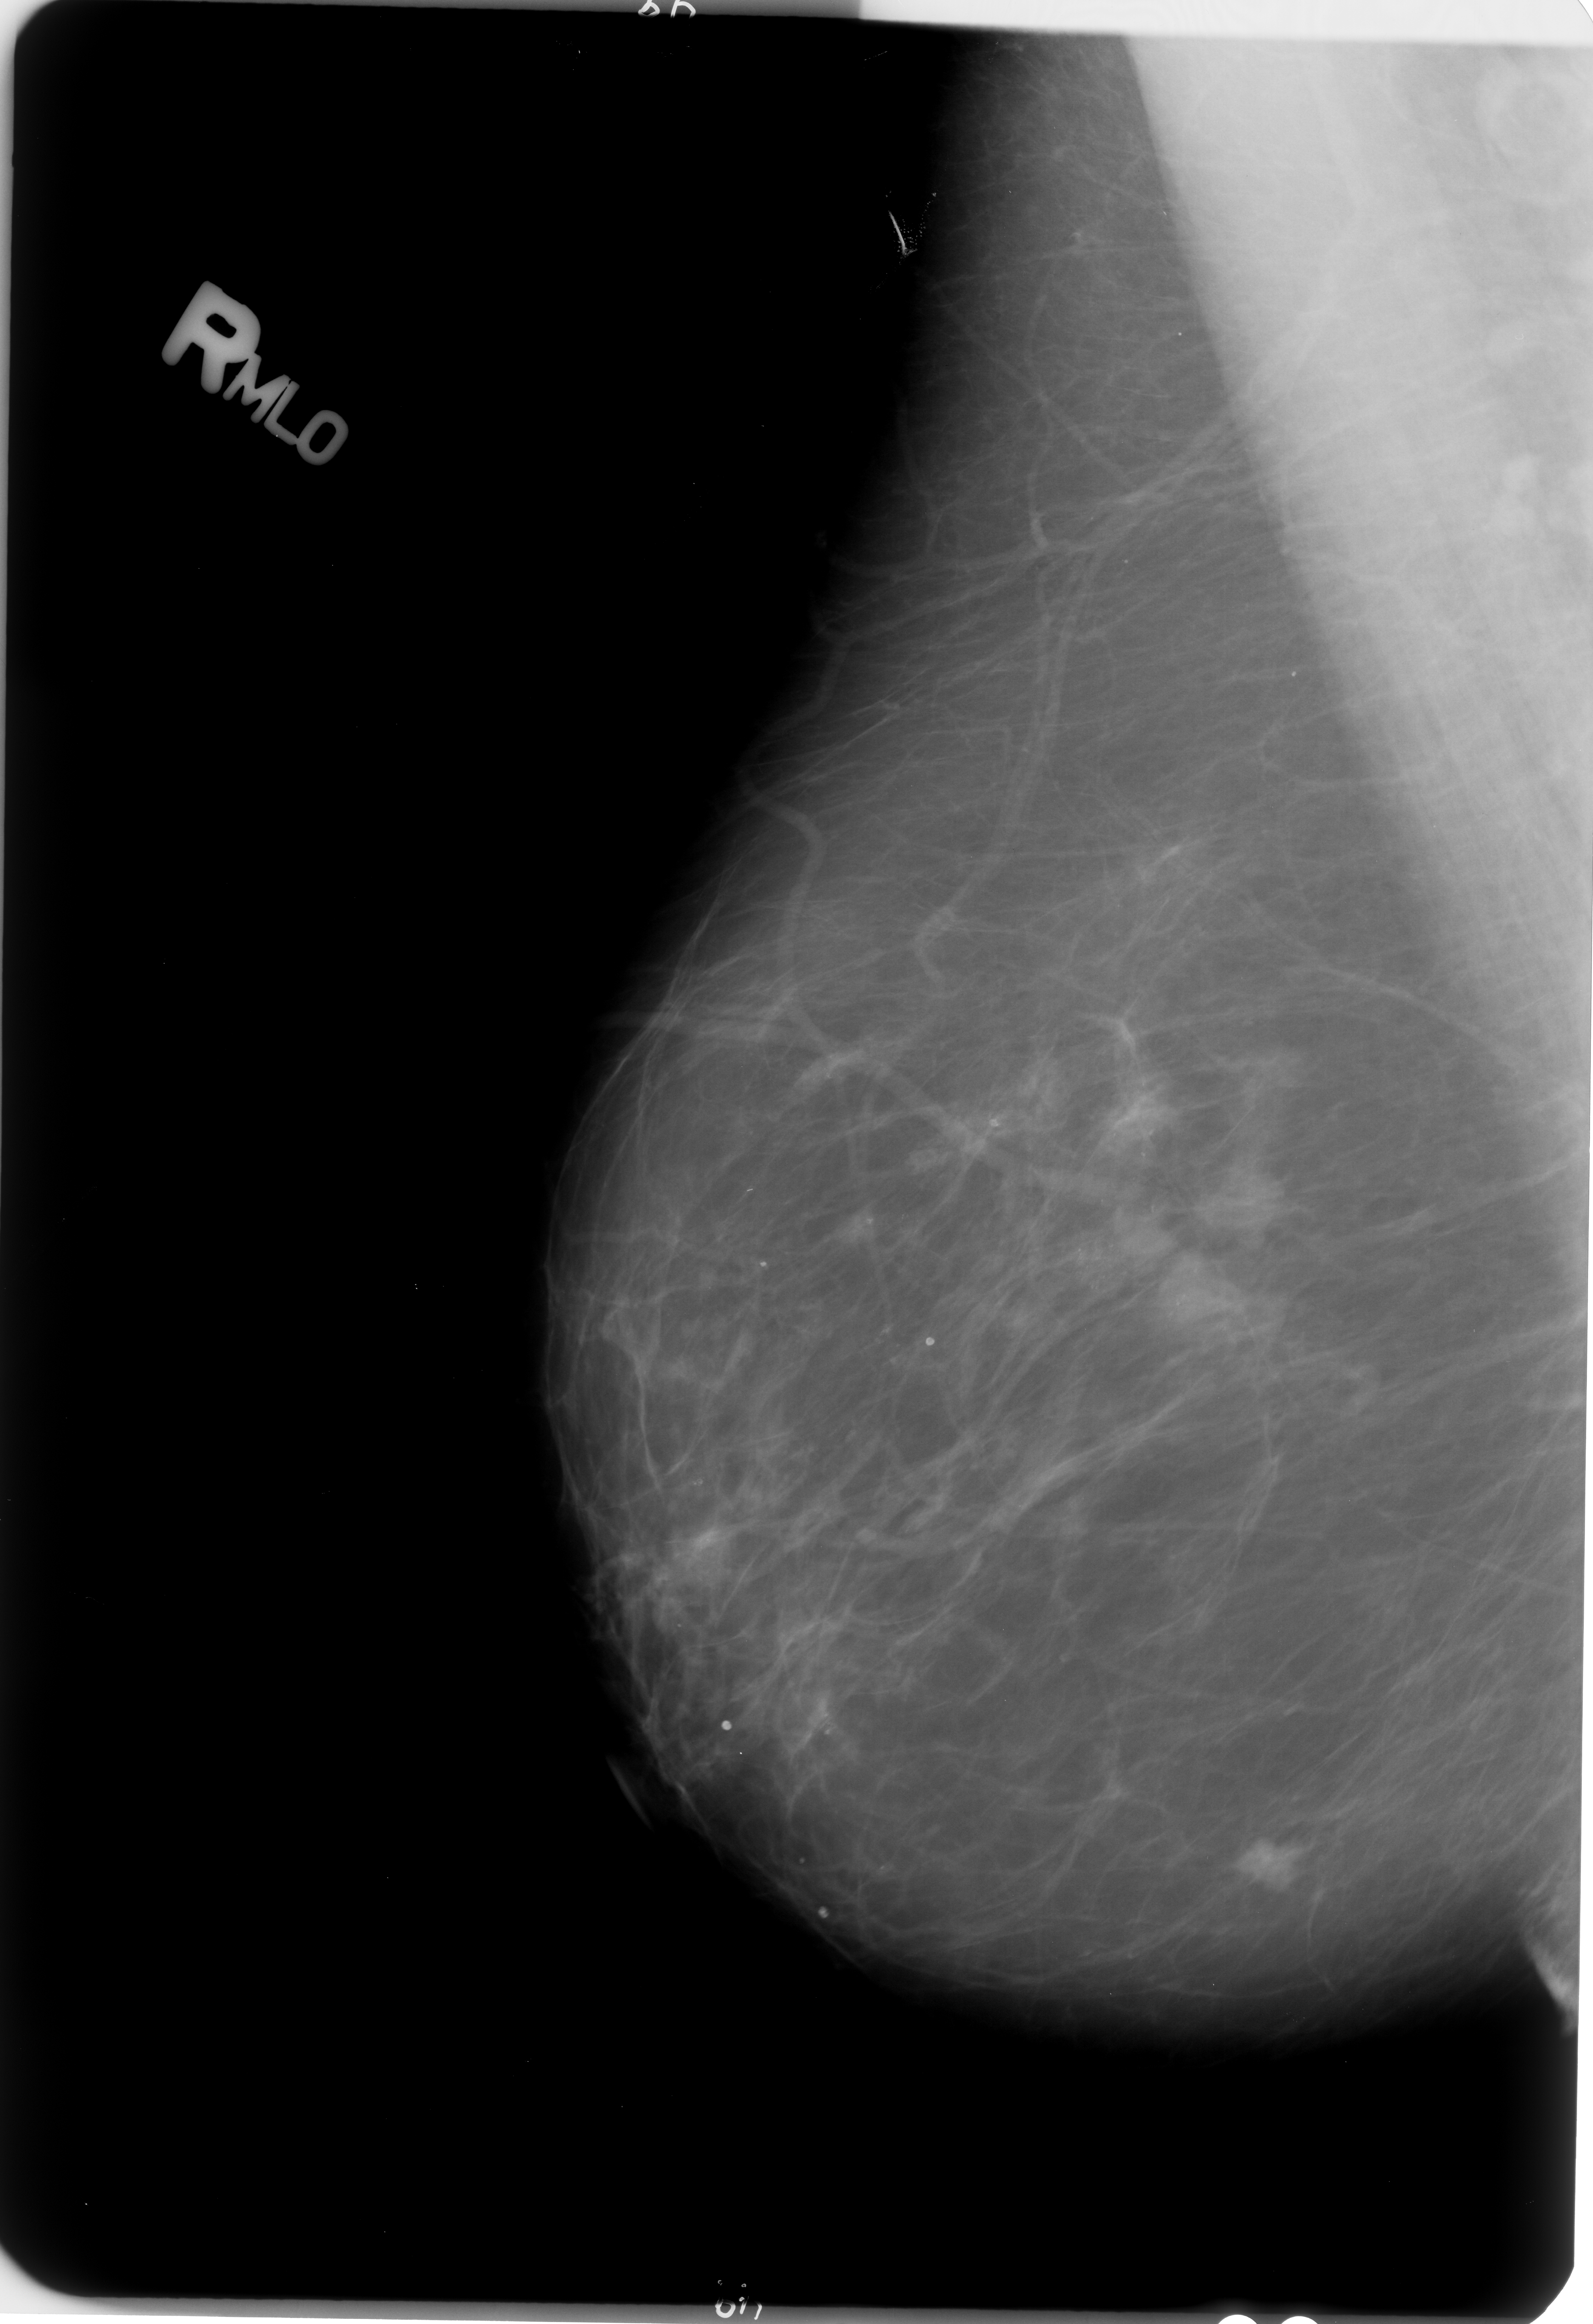
Scanned film-screen mammogram; right breast; MLO view; breast composition: scattered fibroglandular densities (BI-RADS density category 2 of 4); 1593 × 2324 image matrix.
Marked abnormalities (boxes around the expert regions of interest):
- mass, shape irregular, margins microlobulated / spiculated; BI-RADS assessment category 4; subtlety rating 4 on a 1 (subtle) to 5 (obvious) scale; pathology (as recorded): malignant: bounding box <1230,1835,1300,1889> (left, top, right, bottom; pixels)